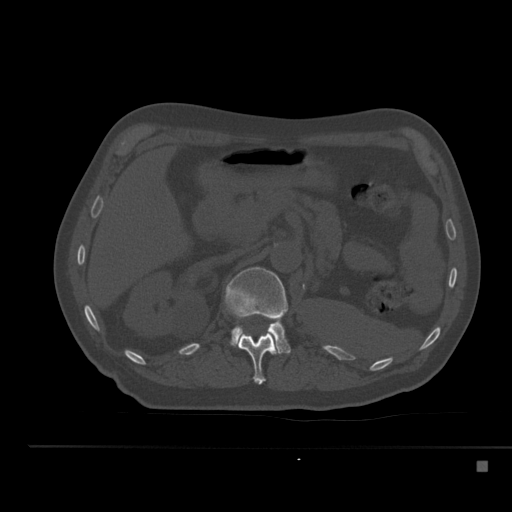
CT including the spine, one axial slice. Slice 219 of 517 in the series (ordered by position). Reconstruction kernel Br40s. Bone window (W 1800 / L 400 HU). 512 × 512 image matrix, field of view 408 × 408 mm. Patient: male, 70 years. From the clinical record (not read from this slice): primary cancer: renal.
Structures marked on this image (semi-automatic segmentation, software-assisted and operator-edited):
- L1 vertebra: box from (x=225, y=267) to (x=291, y=354) px
- T12 vertebra: (x=237, y=332)–(x=277, y=385)